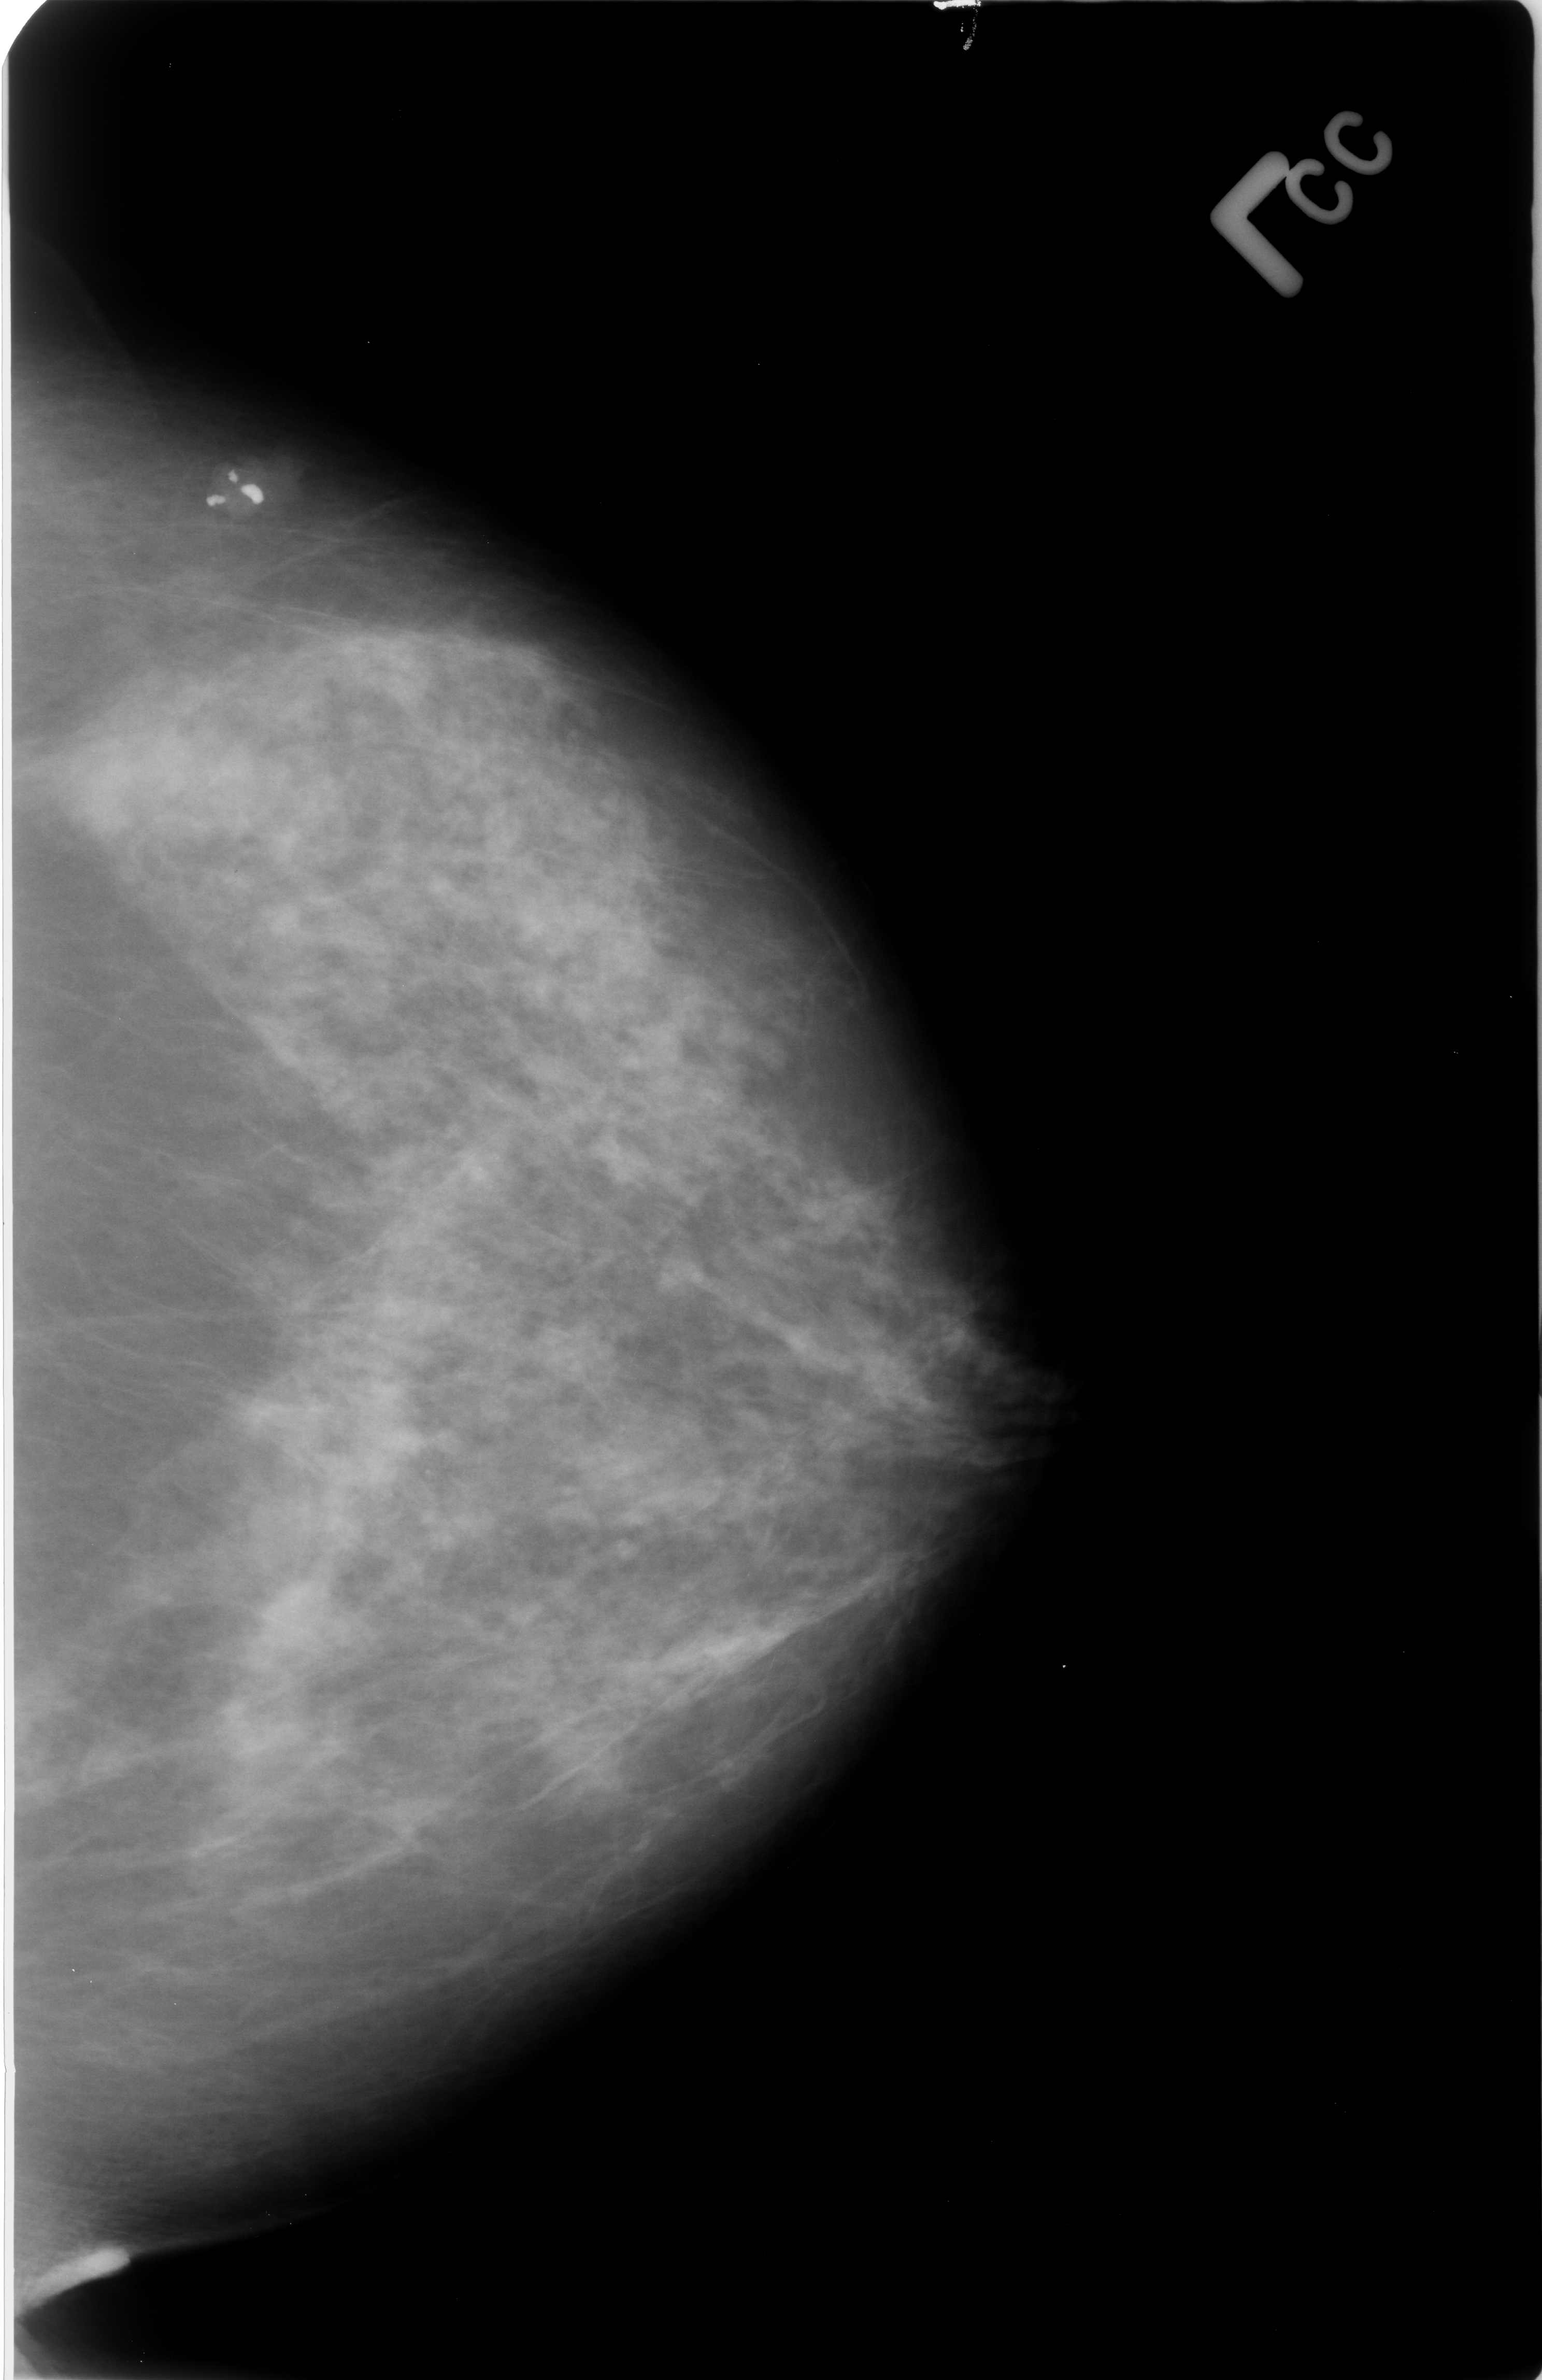
Scanned film-screen mammogram; left breast; craniocaudal (CC) view; 1542 × 2380 image matrix.
Marked abnormalities (boxes around the expert regions of interest):
- calcifications, morphology coarse; BI-RADS assessment category 2; benign; no additional work-up was recommended (outcome (as recorded, no biopsy): benign without callback): box from (x=198, y=451) to (x=295, y=523) px